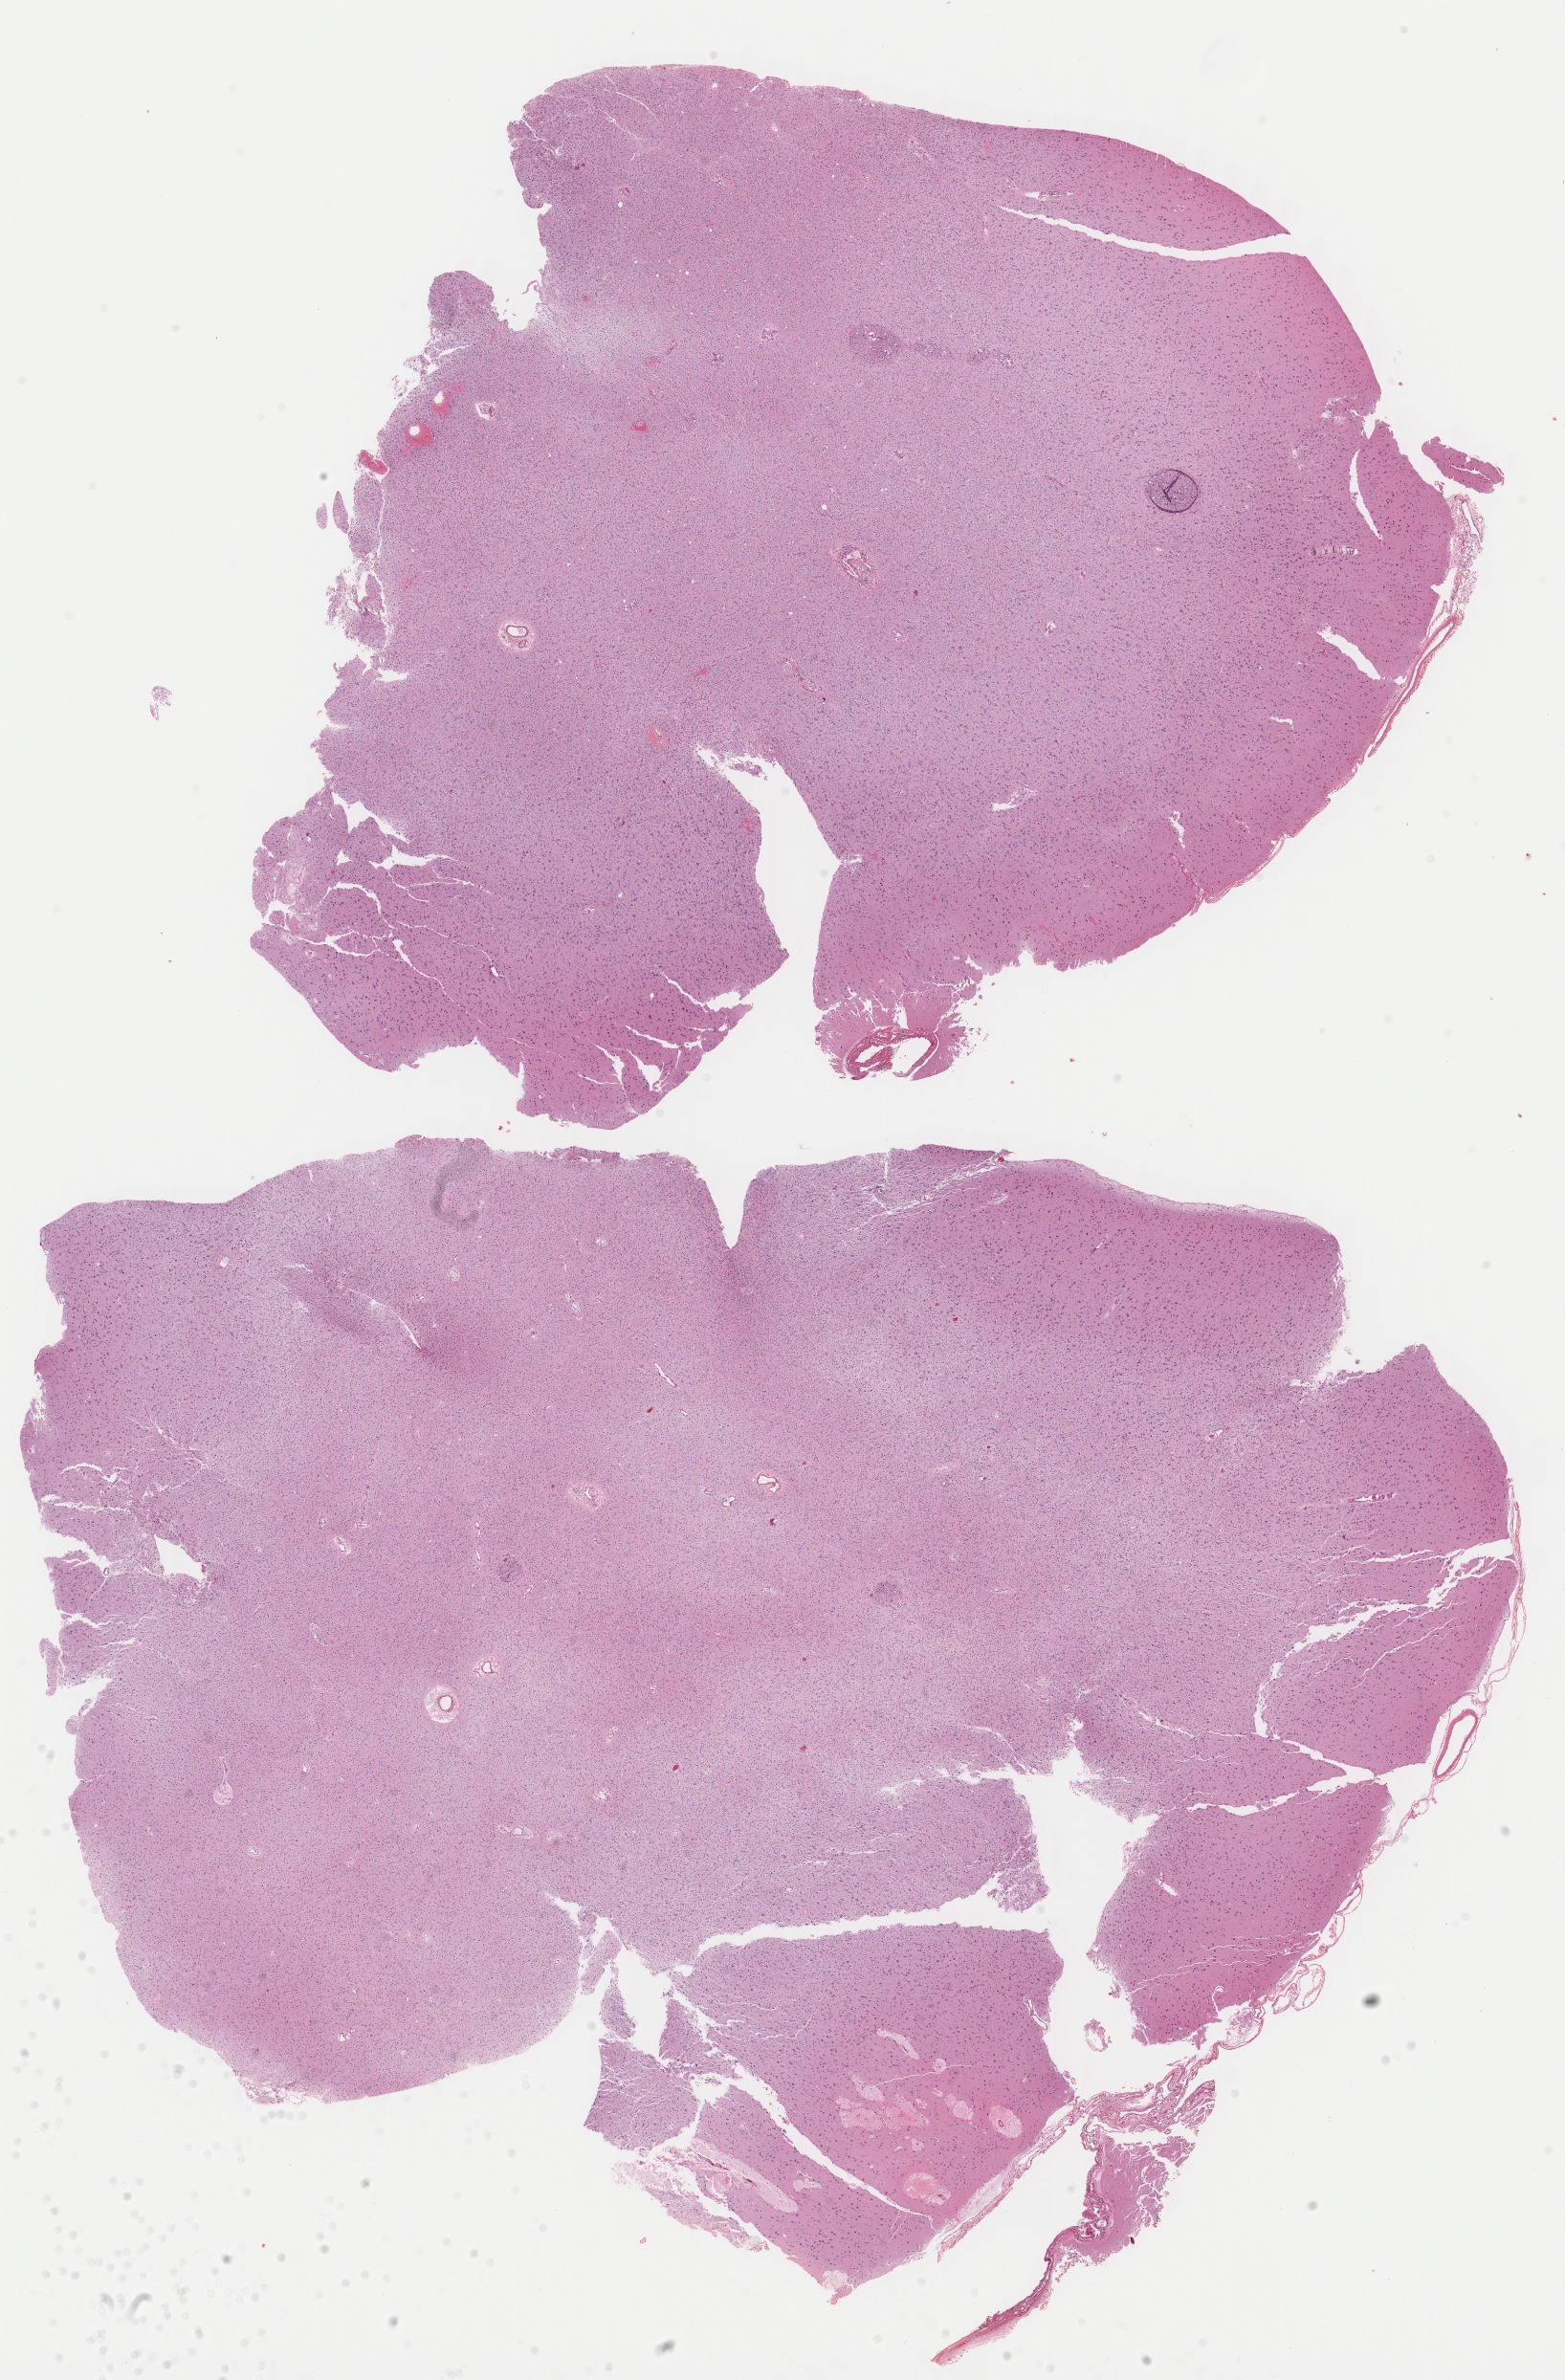
Digitized Hematoxylin and eosin (H&E) stained tissue section (whole slide), low-resolution overview of the scanned area, about 12.9 x 19.6 mm (acquisition: 40x scan). Formalin-fixed paraffin-embedded (FFPE) diagnostic section. Primary tumour sample from the brain. Male, age 17 years at initial diagnosis. Histologic grade: G2 (moderately differentiated).
Laterality: left. Pathologic diagnosis: Oligodendroglioma, NOS (cerebrum).